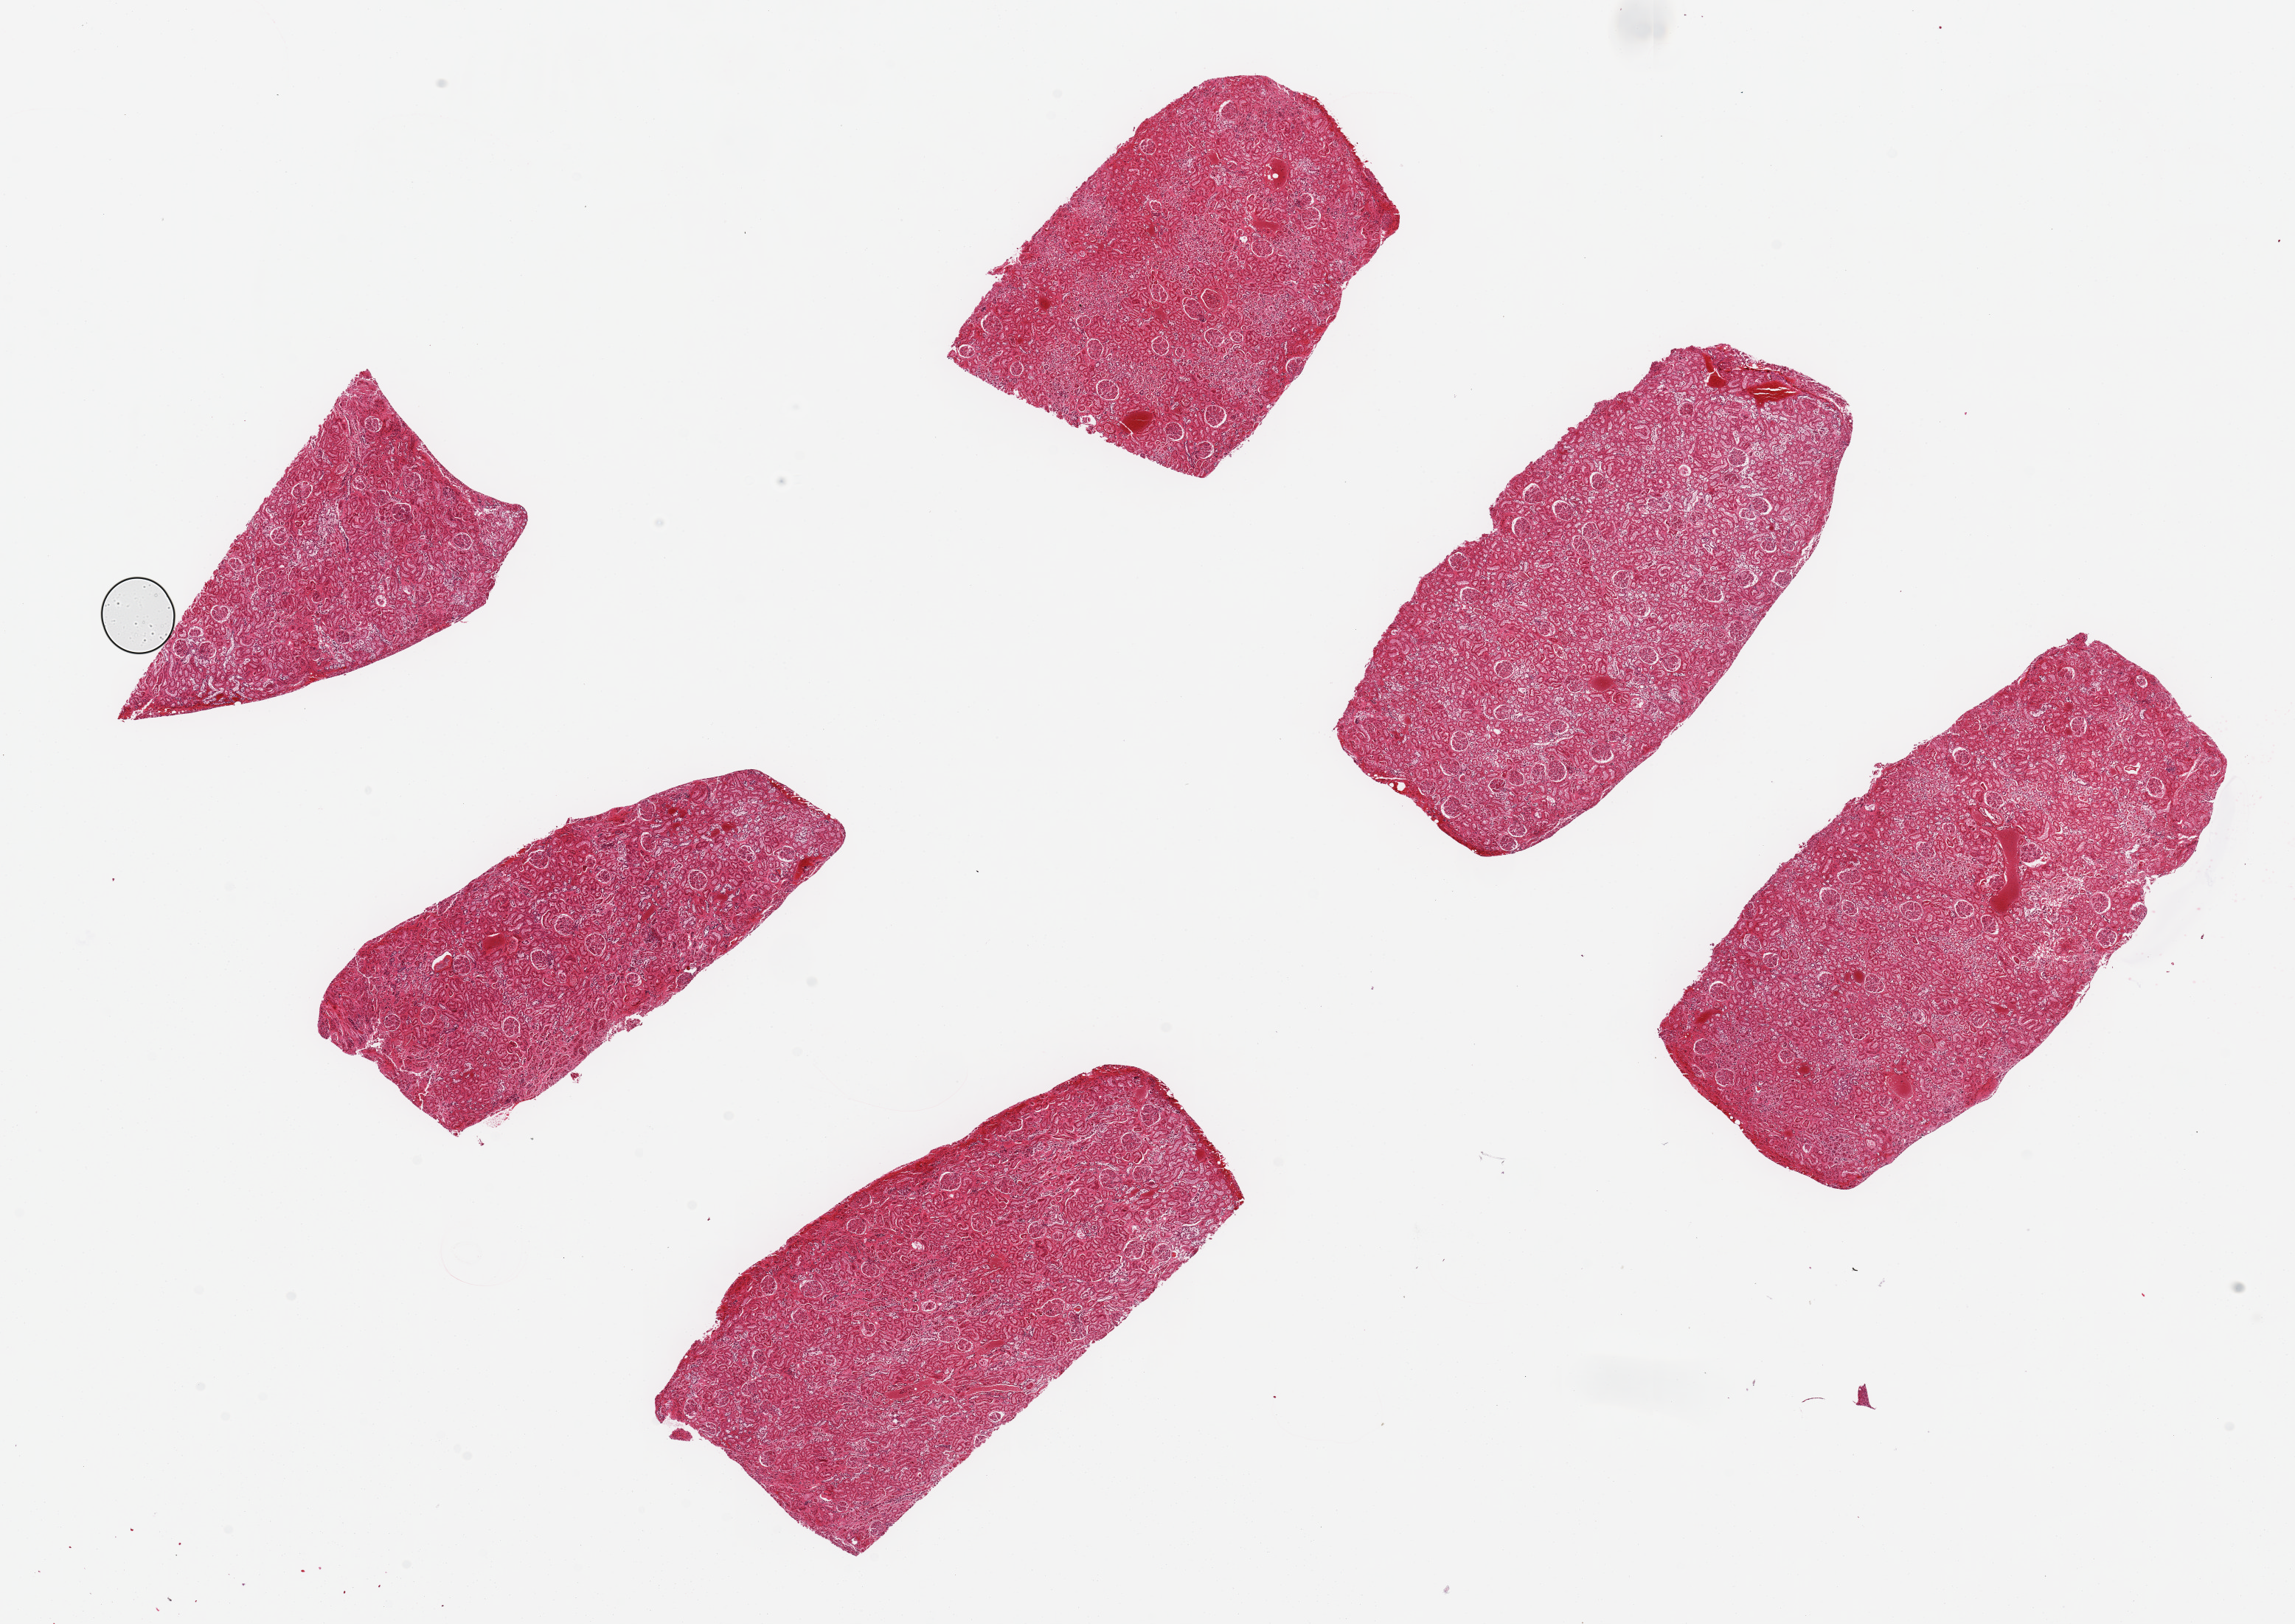
Whole-slide image, H&E stain, brightfield, a low-resolution overview of the entire scanned area, about 24.6 x 17.4 mm (acquisition: 20x scan); PAXgene-fixed, paraffin-embedded tissue; target tissue: renal cortex; tissue donor sample. Donor: female.
* review note (as recorded): 6 ~6.3x3mm pieces. Tubules badly autolyzed